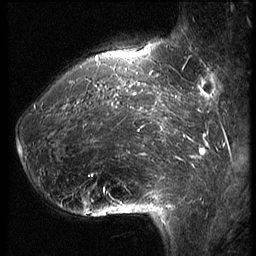
Breast MRI (dynamic contrast-enhanced), one sagittal slice. Slice 16 of 62 in the series (ordered by position). 3 images stored at this slice position (order not interpretable as contrast timing). 1.5 T. TE 4.2 ms, TR 9 ms. 256 × 256 image matrix, field of view 180 × 180 mm. Female patient, age 39 years. From the clinical record (not read from this slice): setting: breast cancer imaged before/during neoadjuvant chemotherapy; receptor status: HER2-positive.
Structures marked on this image (semi-automatically segmented with operator editing):
- analysis volume of interest (the breast-tissue region the enhancement analysis was run in; not a lesion): box from (x=18, y=64) to (x=171, y=228) px
- tumour enhancement mask (voxels above the 140 % enhancement threshold inside the analysis volume of interest): (x=19, y=82)–(x=170, y=194)